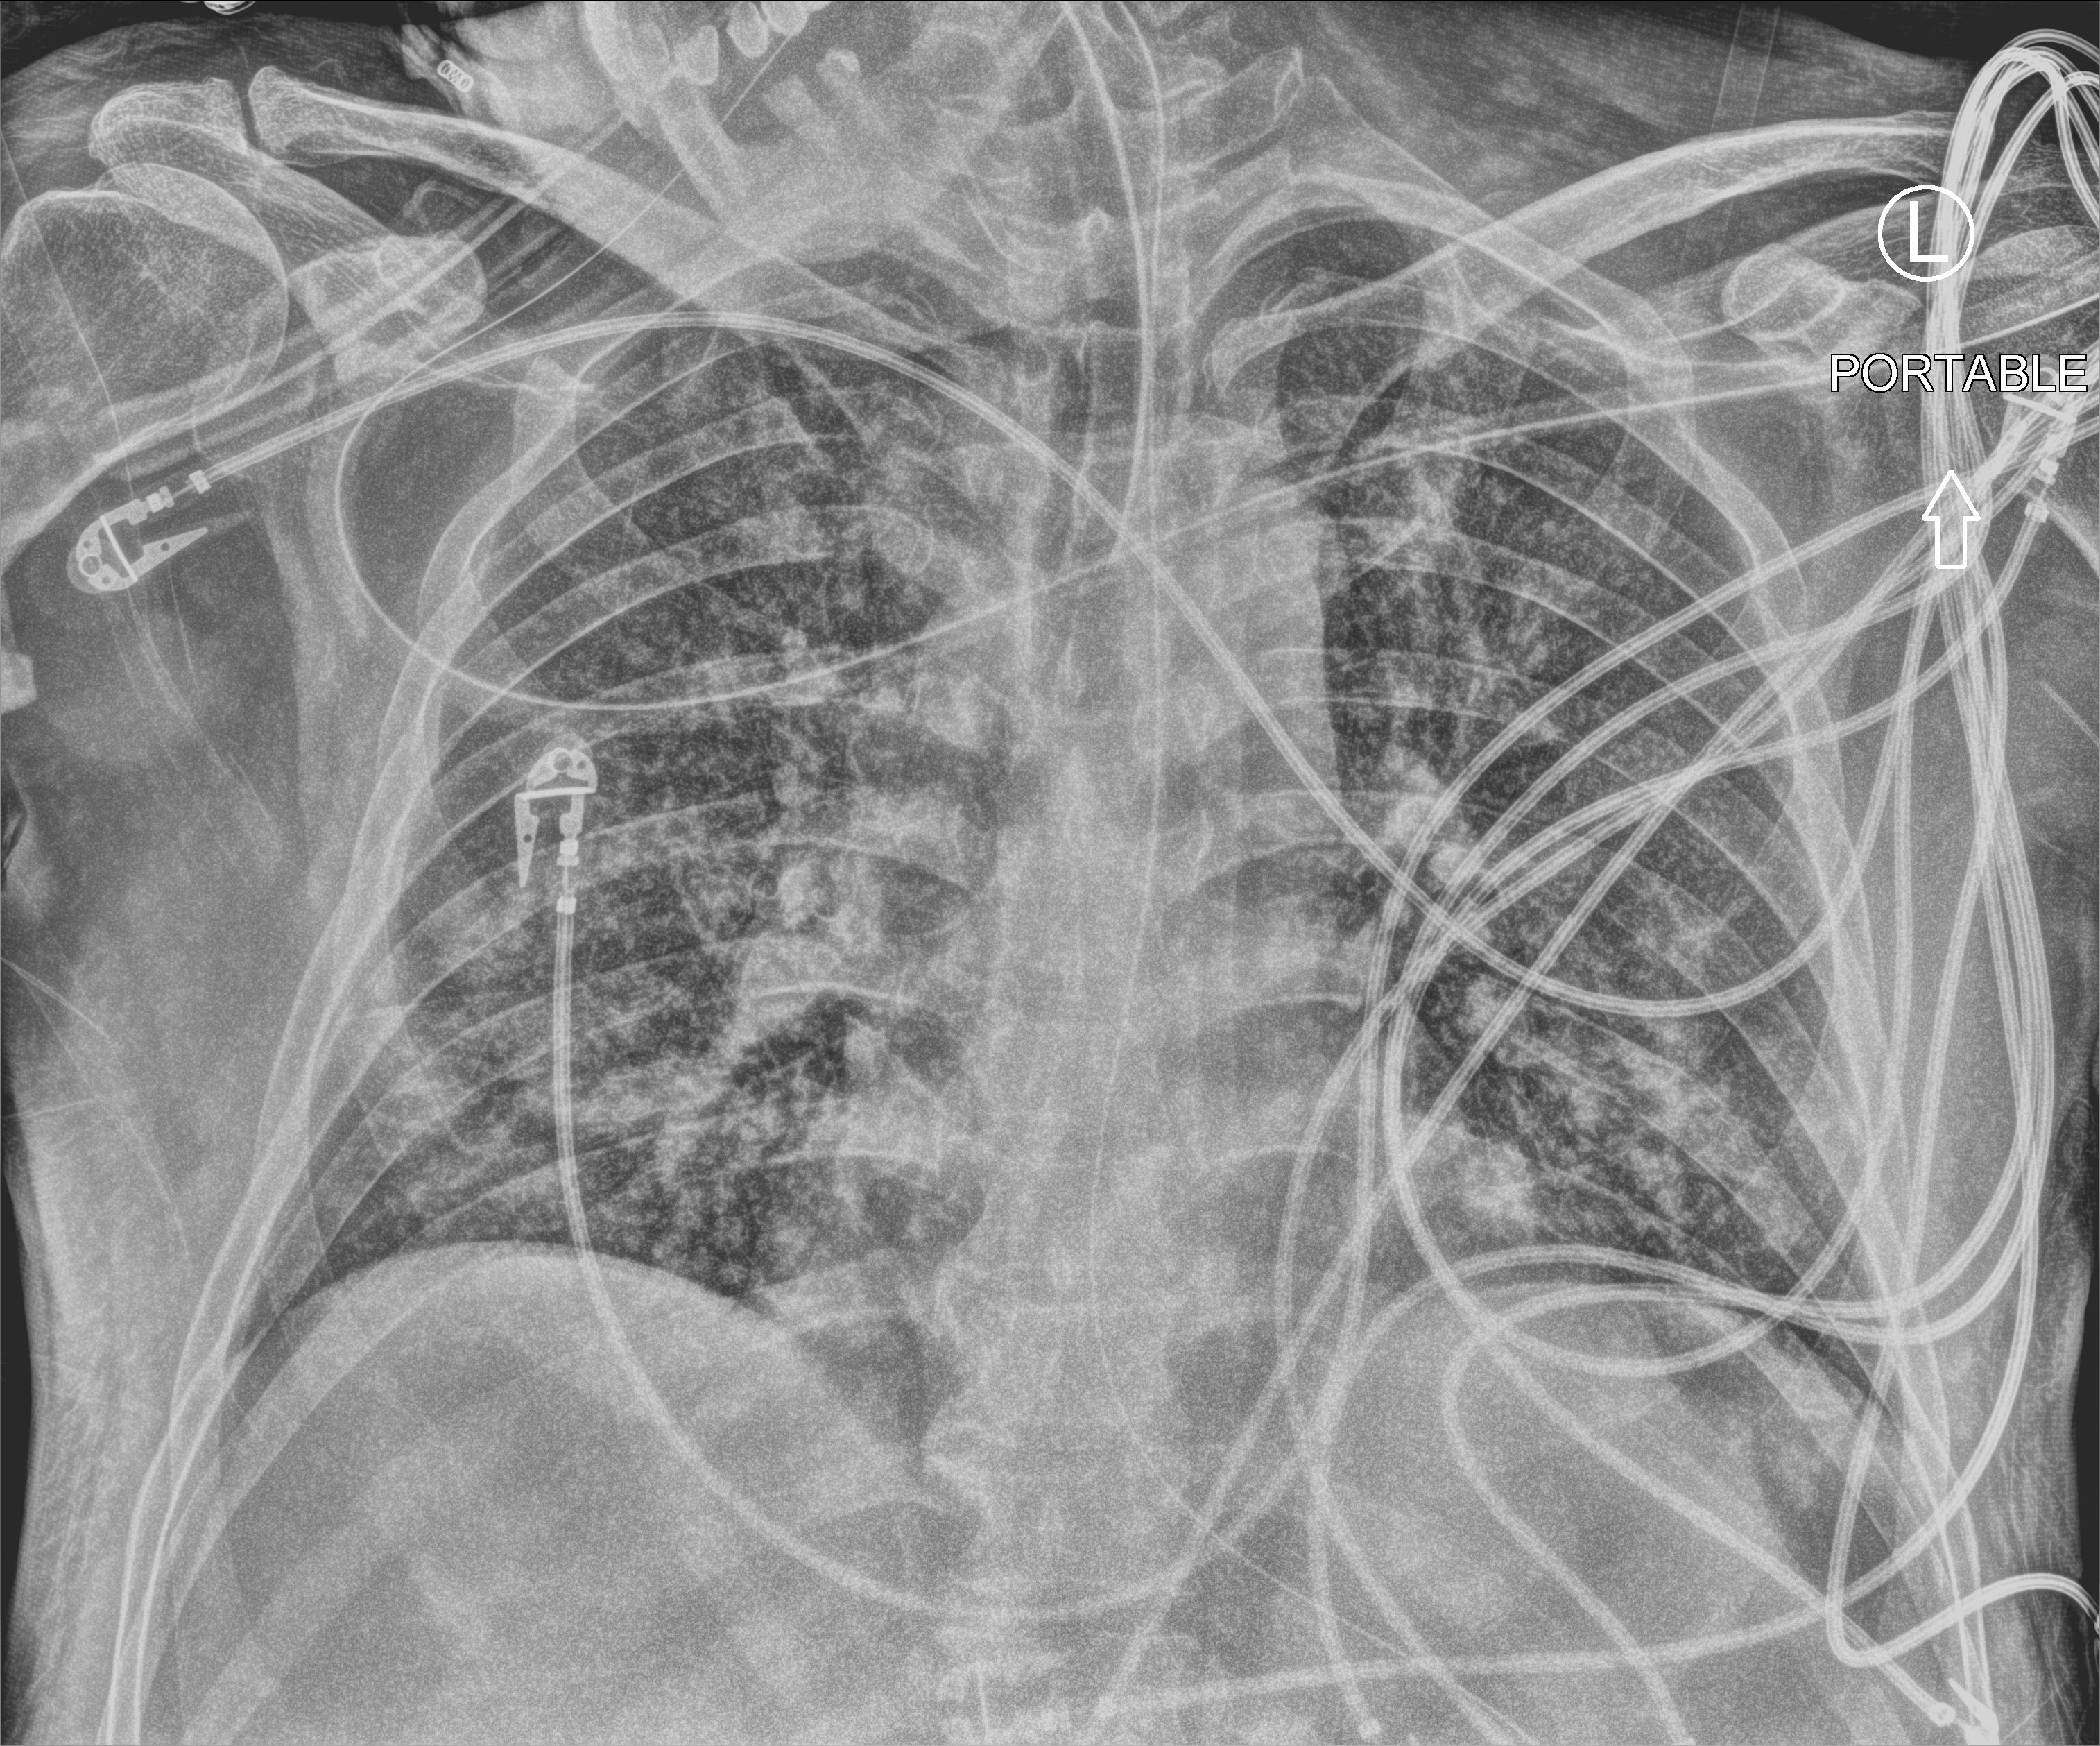
Chest X-ray (portable); anteroposterior (AP) projection. Male patient hospitalised with COVID-19, age 18–59 years.
From the hospital-stay record, not from the radiograph (when in the stay this image was taken is not recorded): mechanically ventilated during this hospital stay: yes; admitted to intensive care during this hospital stay: no.